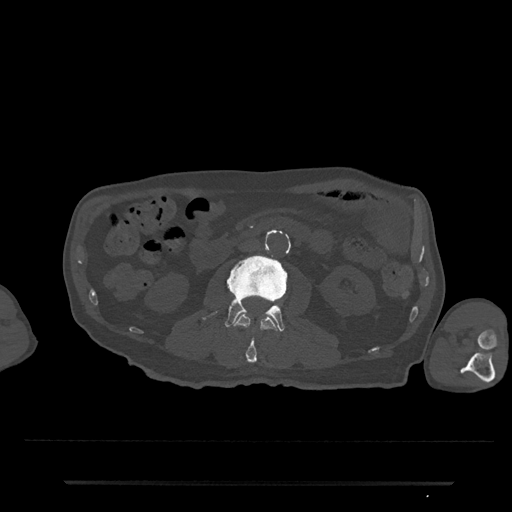
CT including the spine, one axial slice; reconstruction kernel Br40s/3; bone window (W 1800 / L 400 HU); 0.5 mm slice thickness; 512 × 512 image matrix, field of view 427 × 427 mm. Patient: male, 74 years. From the clinical record (not read from this slice): primary cancer: prostate.
Annotated regions visible in this slice (semi-automatic segmentation, software-assisted and operator-edited):
- L2 vertebra: bounding box <234,314,278,363> (left, top, right, bottom; pixels)
- L3 vertebra: <202,255,287,332>